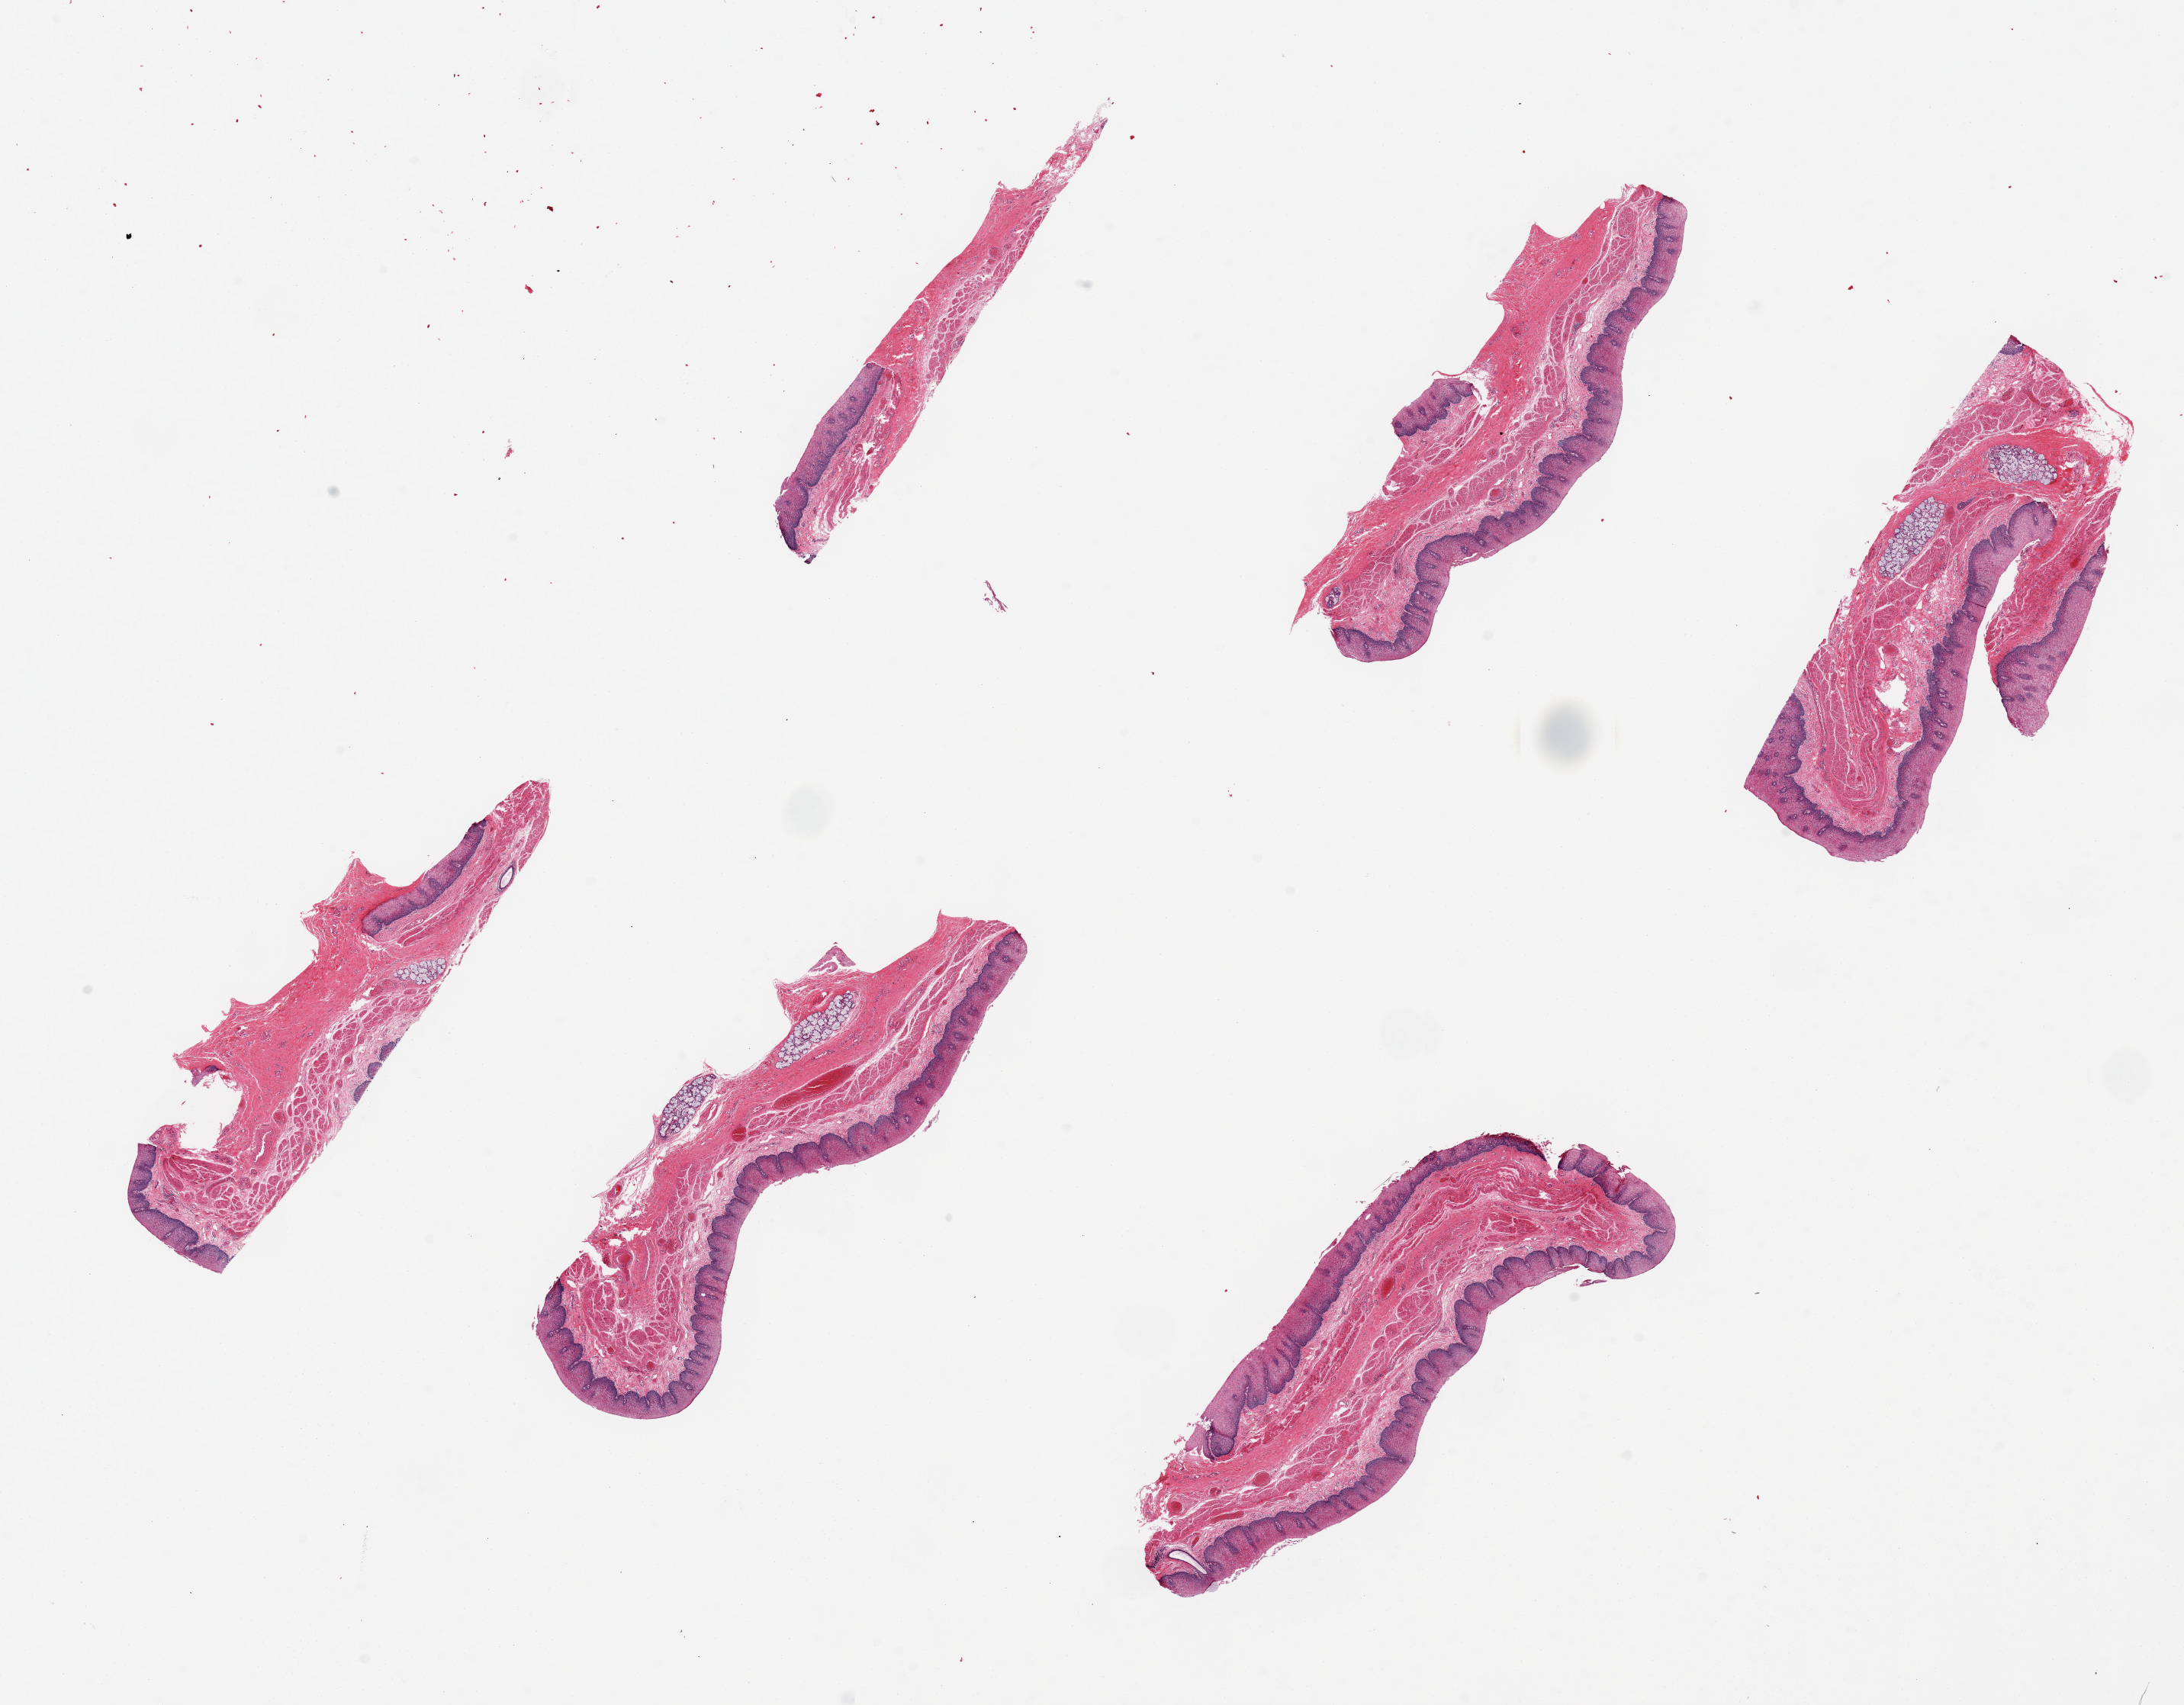
Digitized hematoxylin and eosin (H&E)-stained section, whole scanned area (about 22.6 x 17.7 mm) shown as a low-resolution overview. PAXgene-fixed paraffin-embedded (PFPE) section. Section of esophageal mucous membrane (target tissue). Donor tissue sample. Donor: male.
Reviewer comment on this tissue sample: 6 pieces up to 7x2 mm; slight autolysis of glands; epithelium fine.